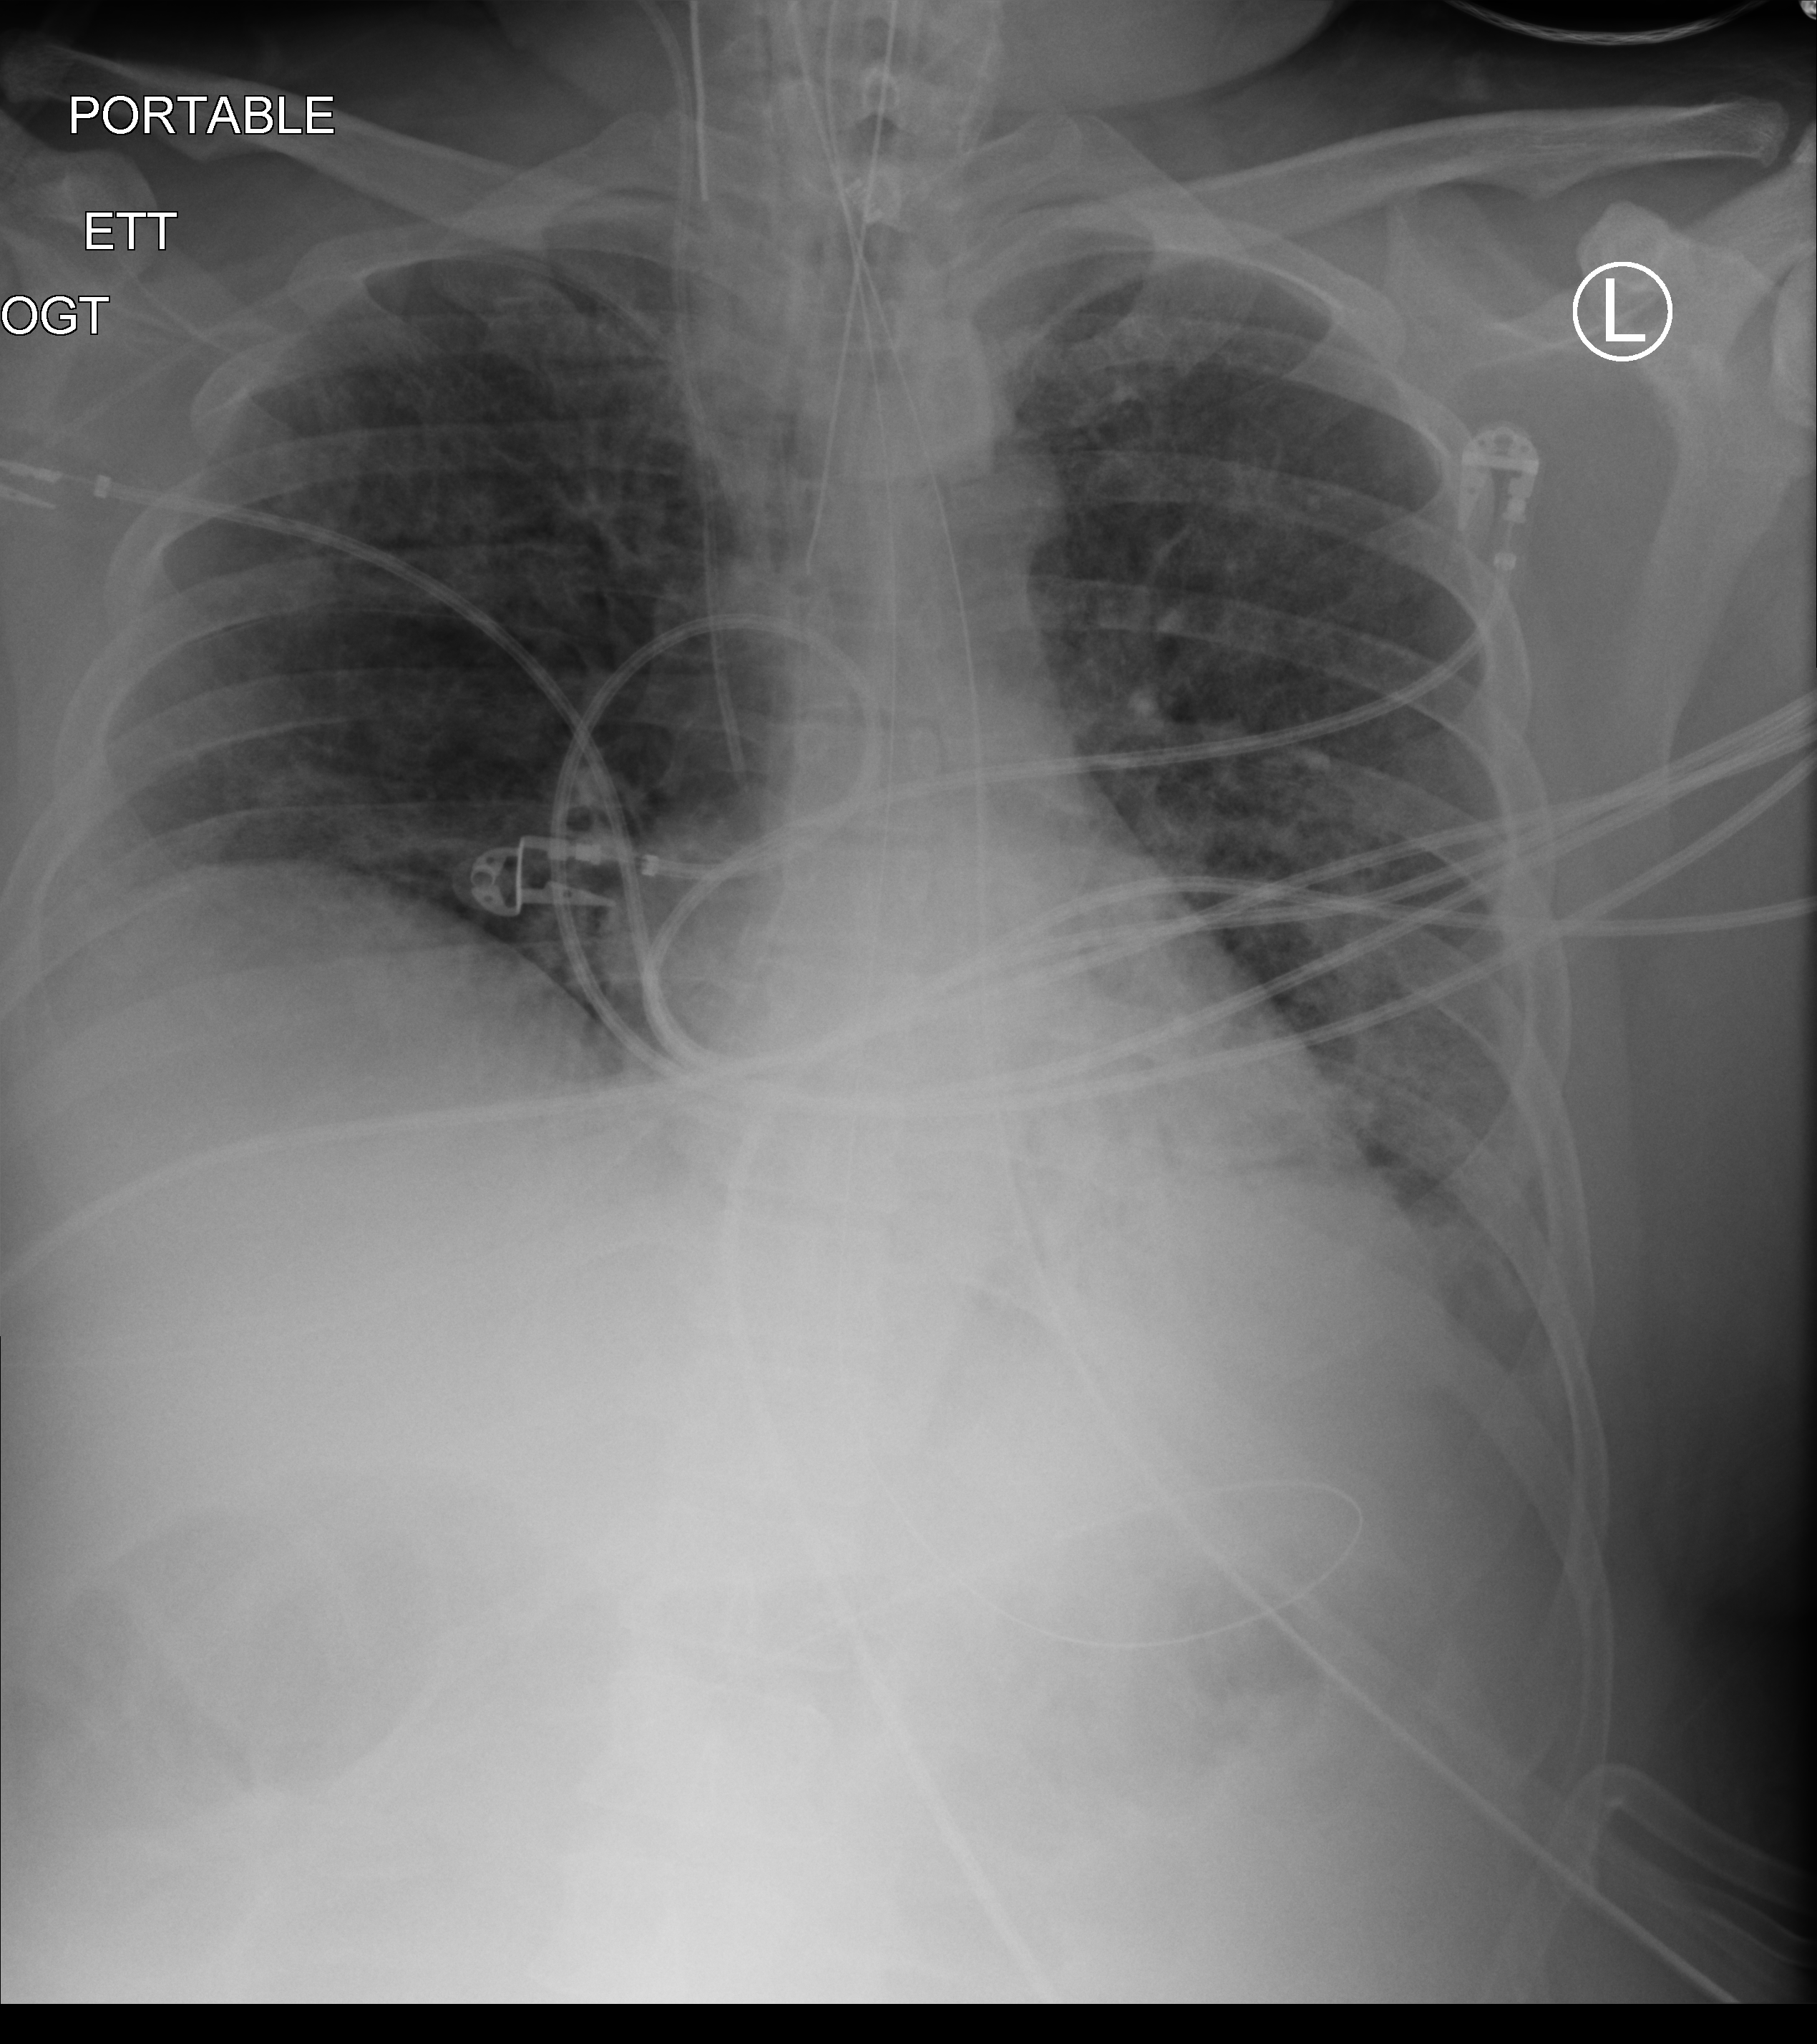
Bedside chest radiograph (computed radiography), anteroposterior (AP) projection. Male patient hospitalised with COVID-19, age 18–59 years.
Admission-level facts for this patient (not findings on this image; timing relative to this image not recorded): admitted to intensive care during this hospital stay: yes; smoking status (admission record): never; mechanically ventilated during this hospital stay: yes.